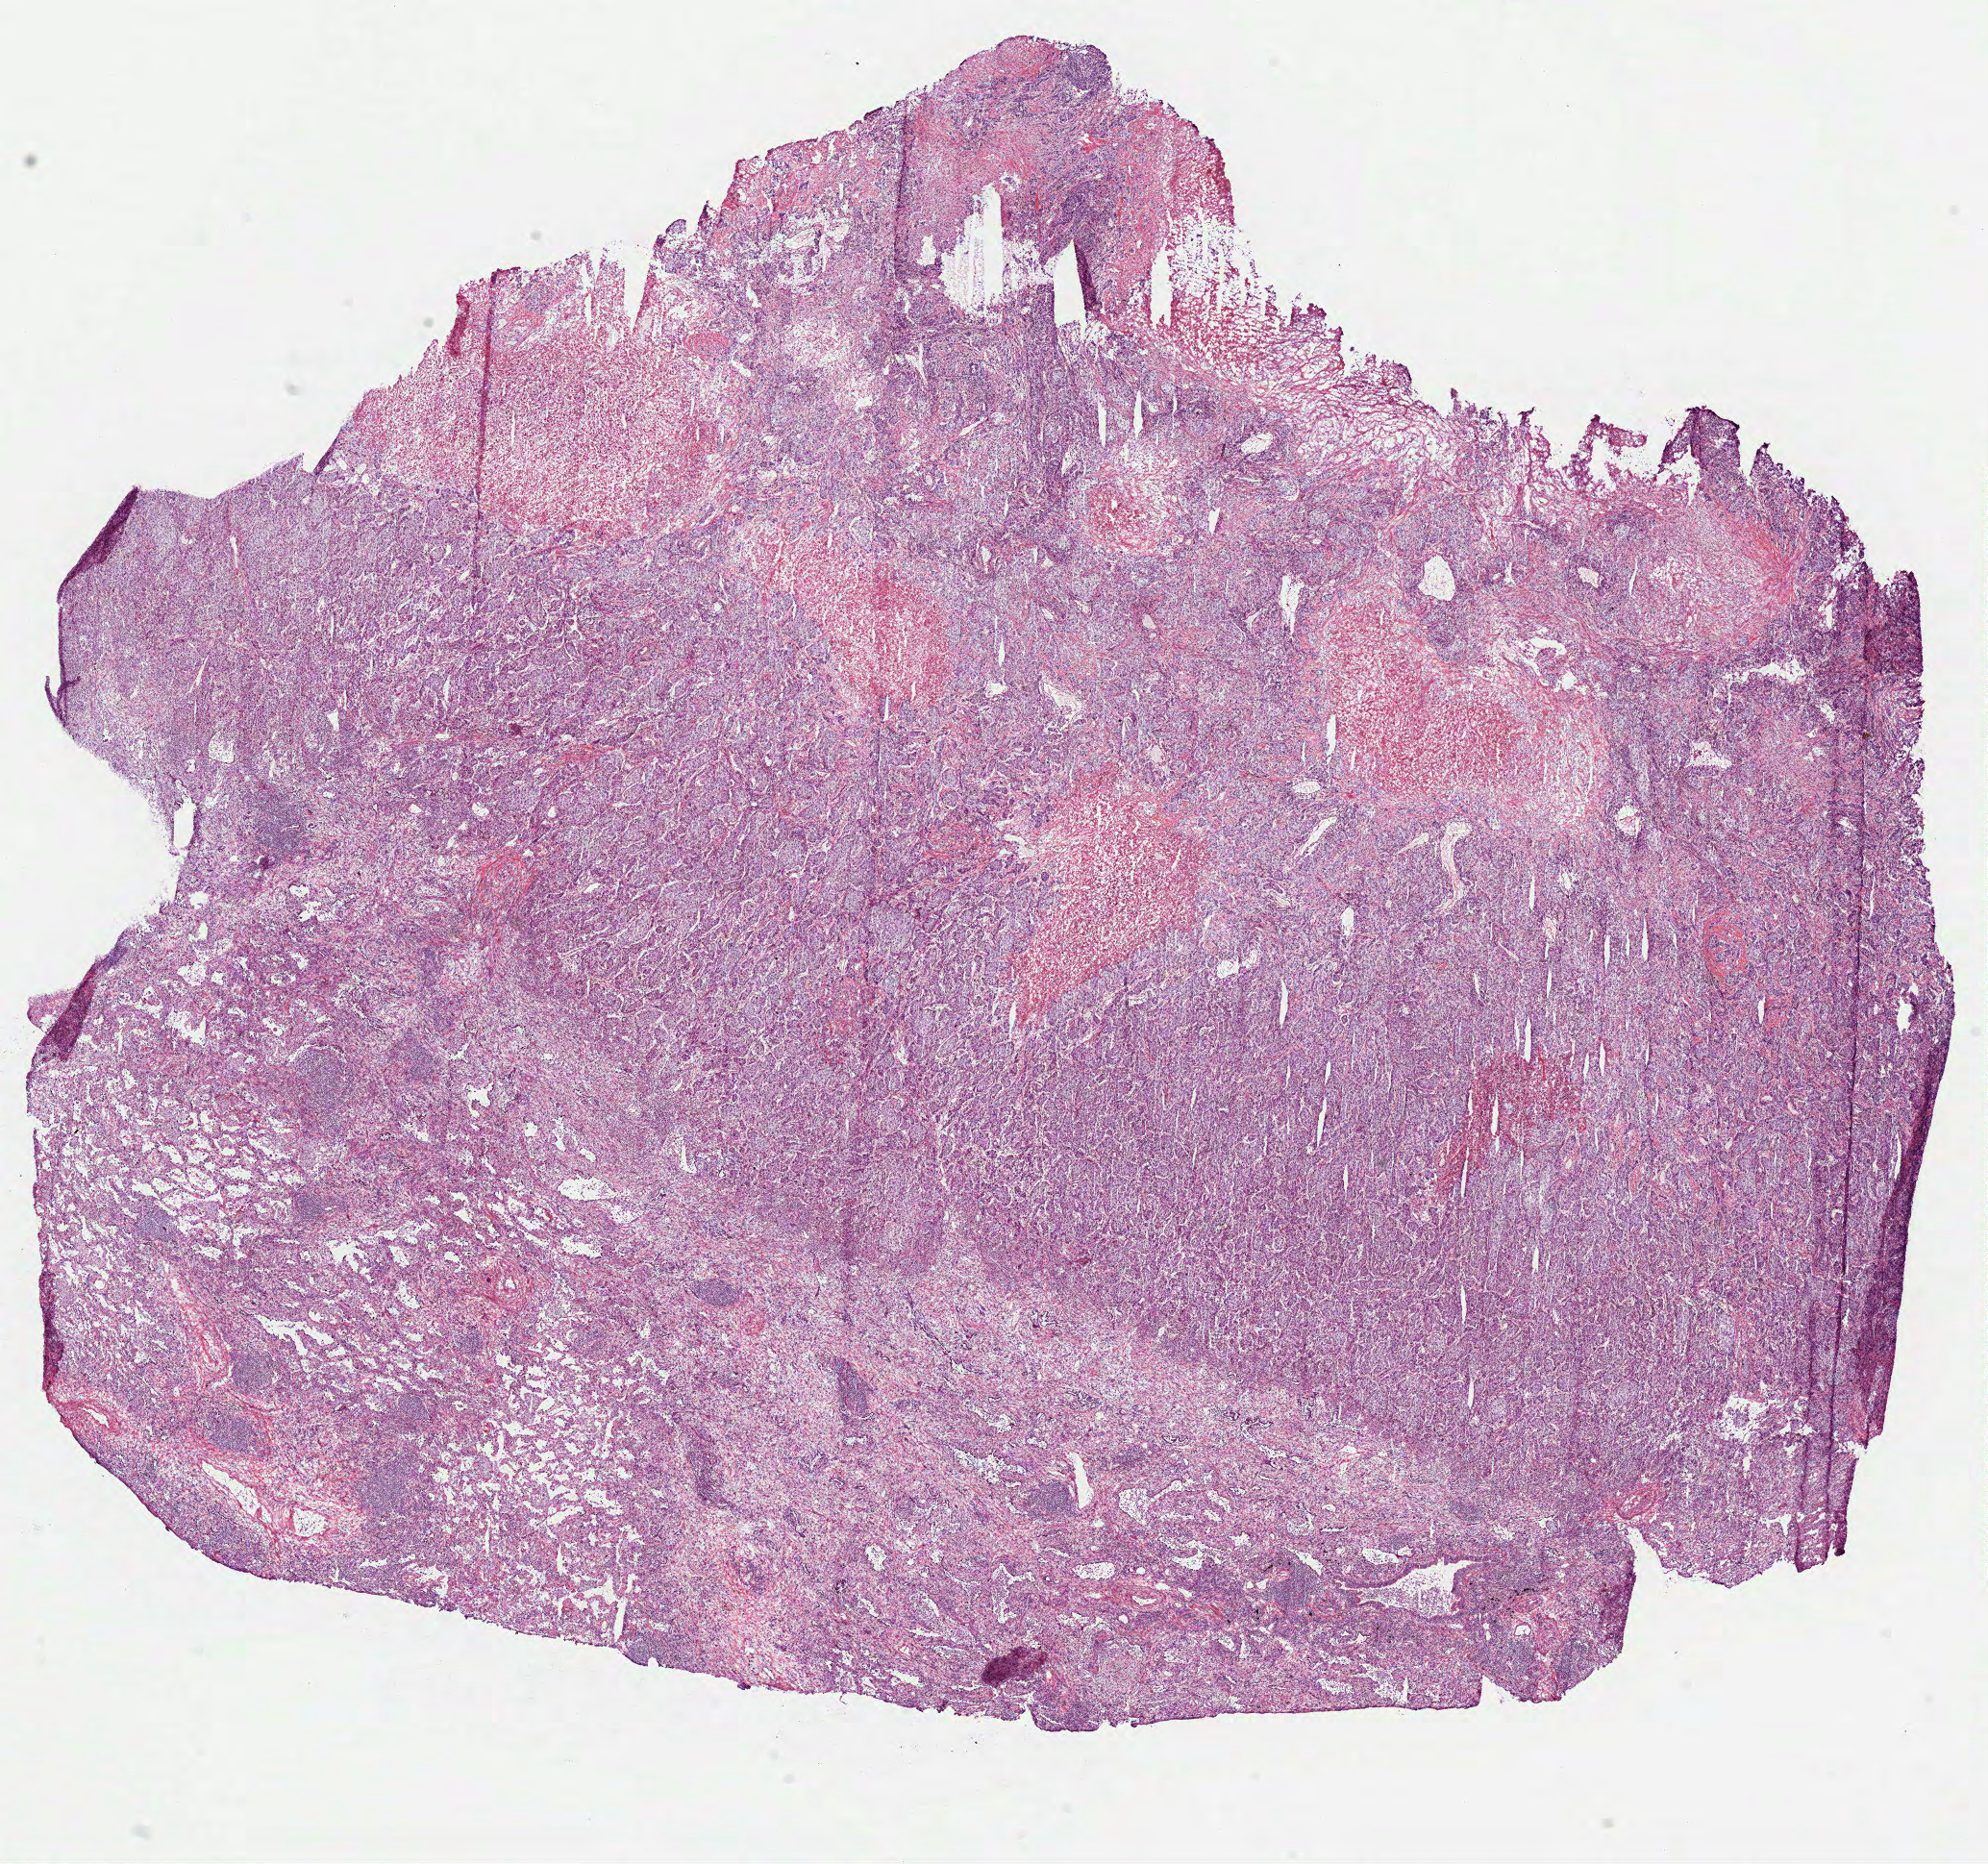
Whole-slide histology image, H&E, shown as a low-resolution overview of the whole scanned area (about 16.7 x 15.6 mm, slide scanned at 40x), frozen section from the bottom of the tissue portion, primary tumour sample from the lung. Male, age 73 years at initial diagnosis. Composition of this section per pathologist review: tumour cells 45%, tumour nuclei 65%, normal cells 25%, stromal cells 15%, necrosis 15%.
AJCC pathologic stage: IB (7th edition). Pathologic diagnosis: Squamous cell carcinoma, NOS (upper lobe, lung).